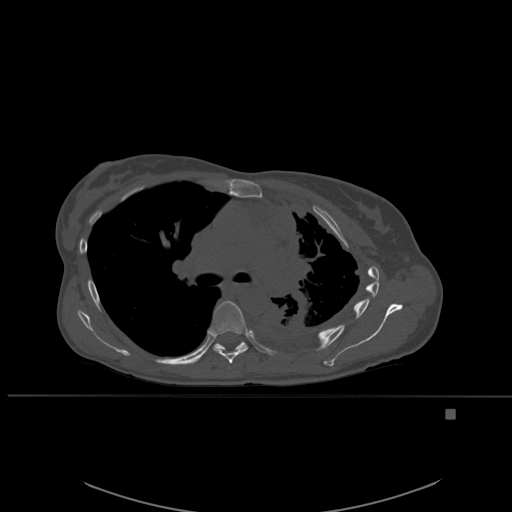
CT including the spine, one axial slice; position 378 of 537 along the scan axis; bone window (W 1800 / L 400 HU); 1.5 mm slice thickness; 512 × 512 image matrix, field of view 440 × 440 mm. Female patient, age 45 years. From the clinical record (not read from this slice): primary cancer: lung.
Outlined on this slice (semi-automatic segmentation, software-assisted and operator-edited):
- T6 vertebra: bounding box <210,301,248,364> (left, top, right, bottom; pixels)
- T7 vertebra: <215,341,248,350>